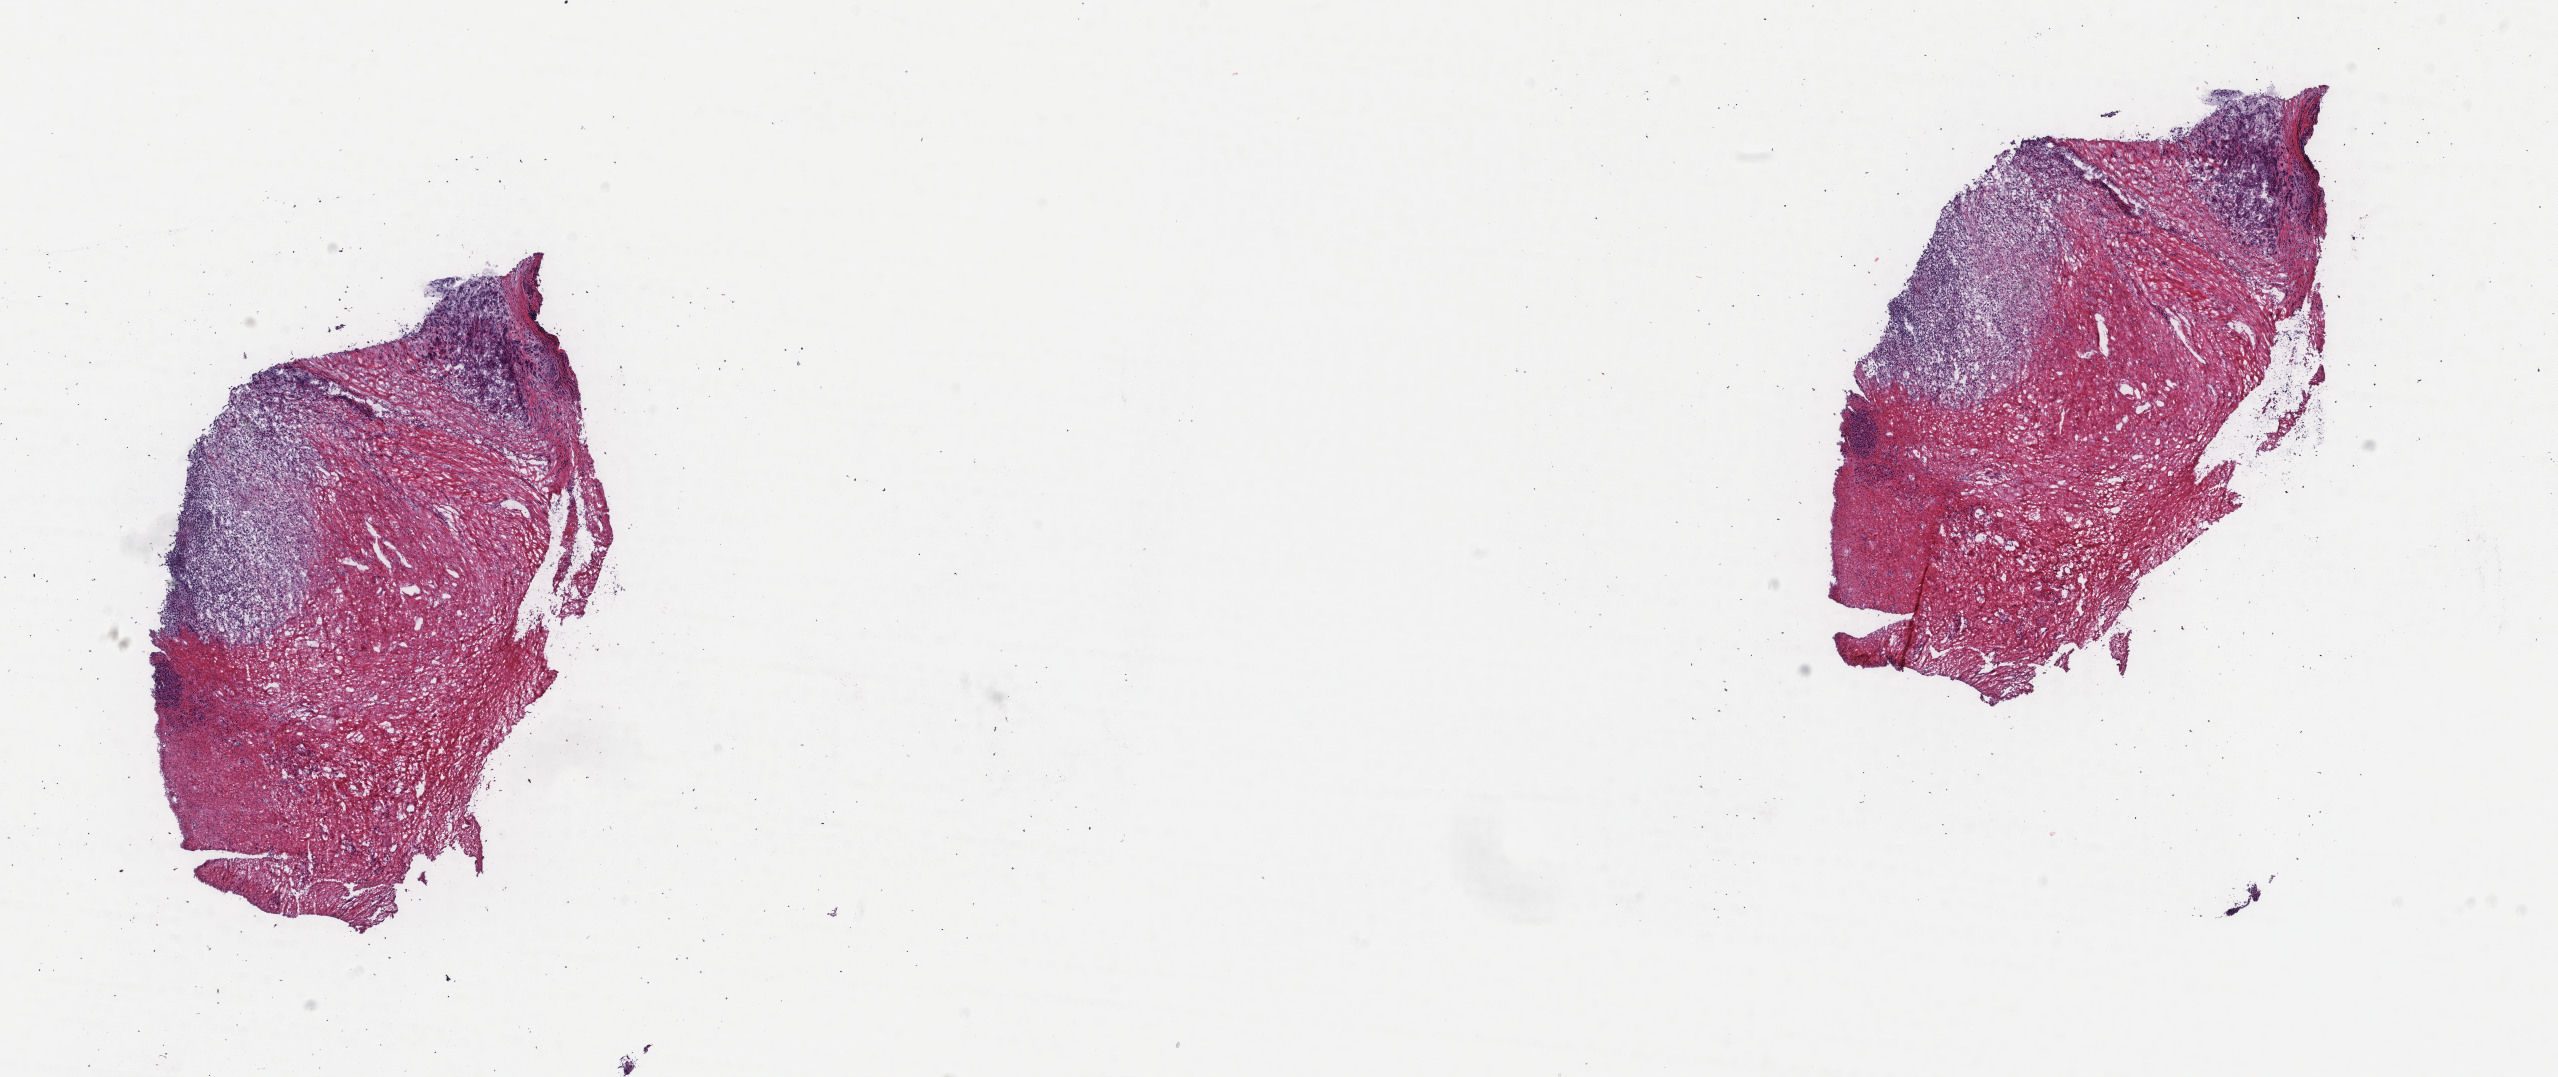
H&E-stained whole-slide image, shown as a low-resolution overview of the whole scanned area (about 20.3 x 8.5 mm), frozen section, metastatic tumour sample, sampled site not recorded. Female, age 36 years at initial diagnosis. Pathologist review of this section (percent, as recorded): tumour cells 35%, tumour nuclei 60%, normal cells 0%, stromal cells 65%, necrosis 0%. Infiltration values recorded for this section: lymphocyte infiltration 0%, monocyte infiltration 0%, neutrophil infiltration 0%.
This section: metastatic tumour tissue. Patient diagnosis: Malignant melanoma, NOS.